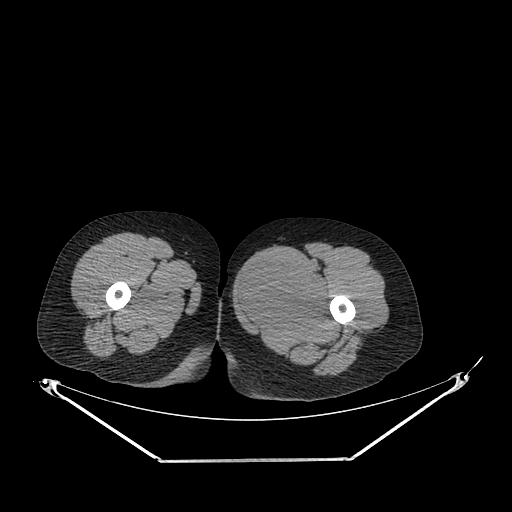
CT of an extremity soft-tissue mass (from a PET/CT study), one axial slice. Slice 240 of 267 in the series (ordered by position). 120 kVp. Soft-tissue window (W 400 / L 40 HU). 3.75 mm slice thickness. 512 × 512 image matrix, field of view 500 × 500 mm. Female patient. From the clinical record (not read from this slice): histological type: pleiomorphic leiomyosarcoma; grade: intermediate; site of the primary tumour: left thigh.
Annotated regions visible in this slice (expert contour drawn on MRI and transferred to this co-registered scan by the dataset authors):
- gross tumour volume including surrounding oedema: bounding box [x1, y1, x2, y2] px = [237, 258, 328, 332]
- gross tumour volume (mass): [237, 260, 327, 330]